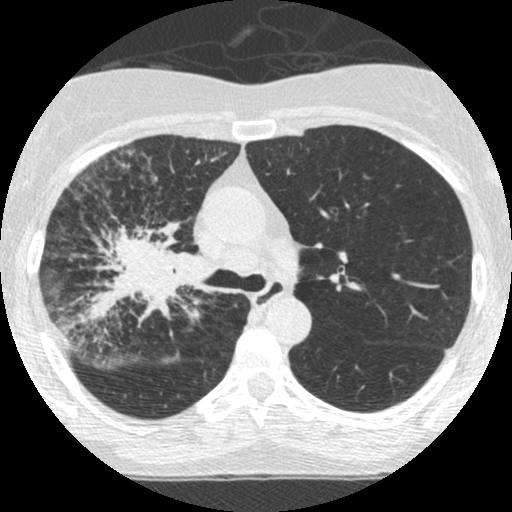
Low-dose screening chest CT, one axial slice; slice 172 of 253 in the series (ordered by position); 120 kVp; lung window (W 1500 / L -600 HU); 512 × 512 image matrix.
Outlined on this slice (outlined manually by an expert reader):
- lesion 2 (tumor, hilum of right lung): bounding box [x1, y1, x2, y2] px = [80, 221, 204, 325]